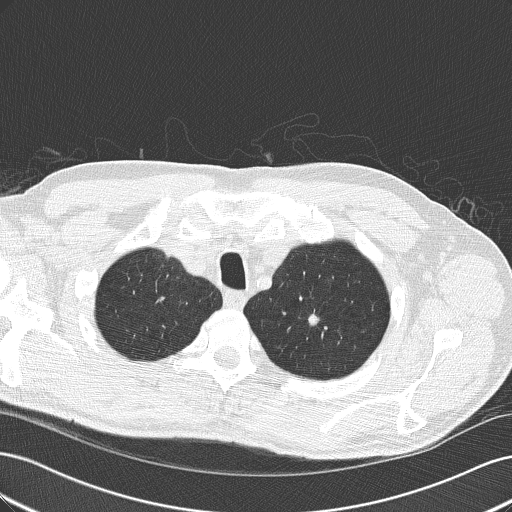
Chest CT (low-dose screening protocol), one axial image. Third screening round (two years after baseline). Lung window (W 1500 / L -600 HU). 2 mm slice thickness. Slice 35 of 192 in the series. Male, age 64 years at enrolment. Former smoker at enrolment.
Lesion marked by an expert reader, bounding box [x1, y1, x2, y2] px = [290, 300, 334, 342]. Screening reader's record for this exam (one nodule recorded; not confirmed to be the boxed lesion): non-calcified nodule or mass ≥4 mm, left upper lobe, 8 × 8 mm, smooth margins, soft tissue attenuation, pre-existing on the prior screen: yes; interval growth: yes.